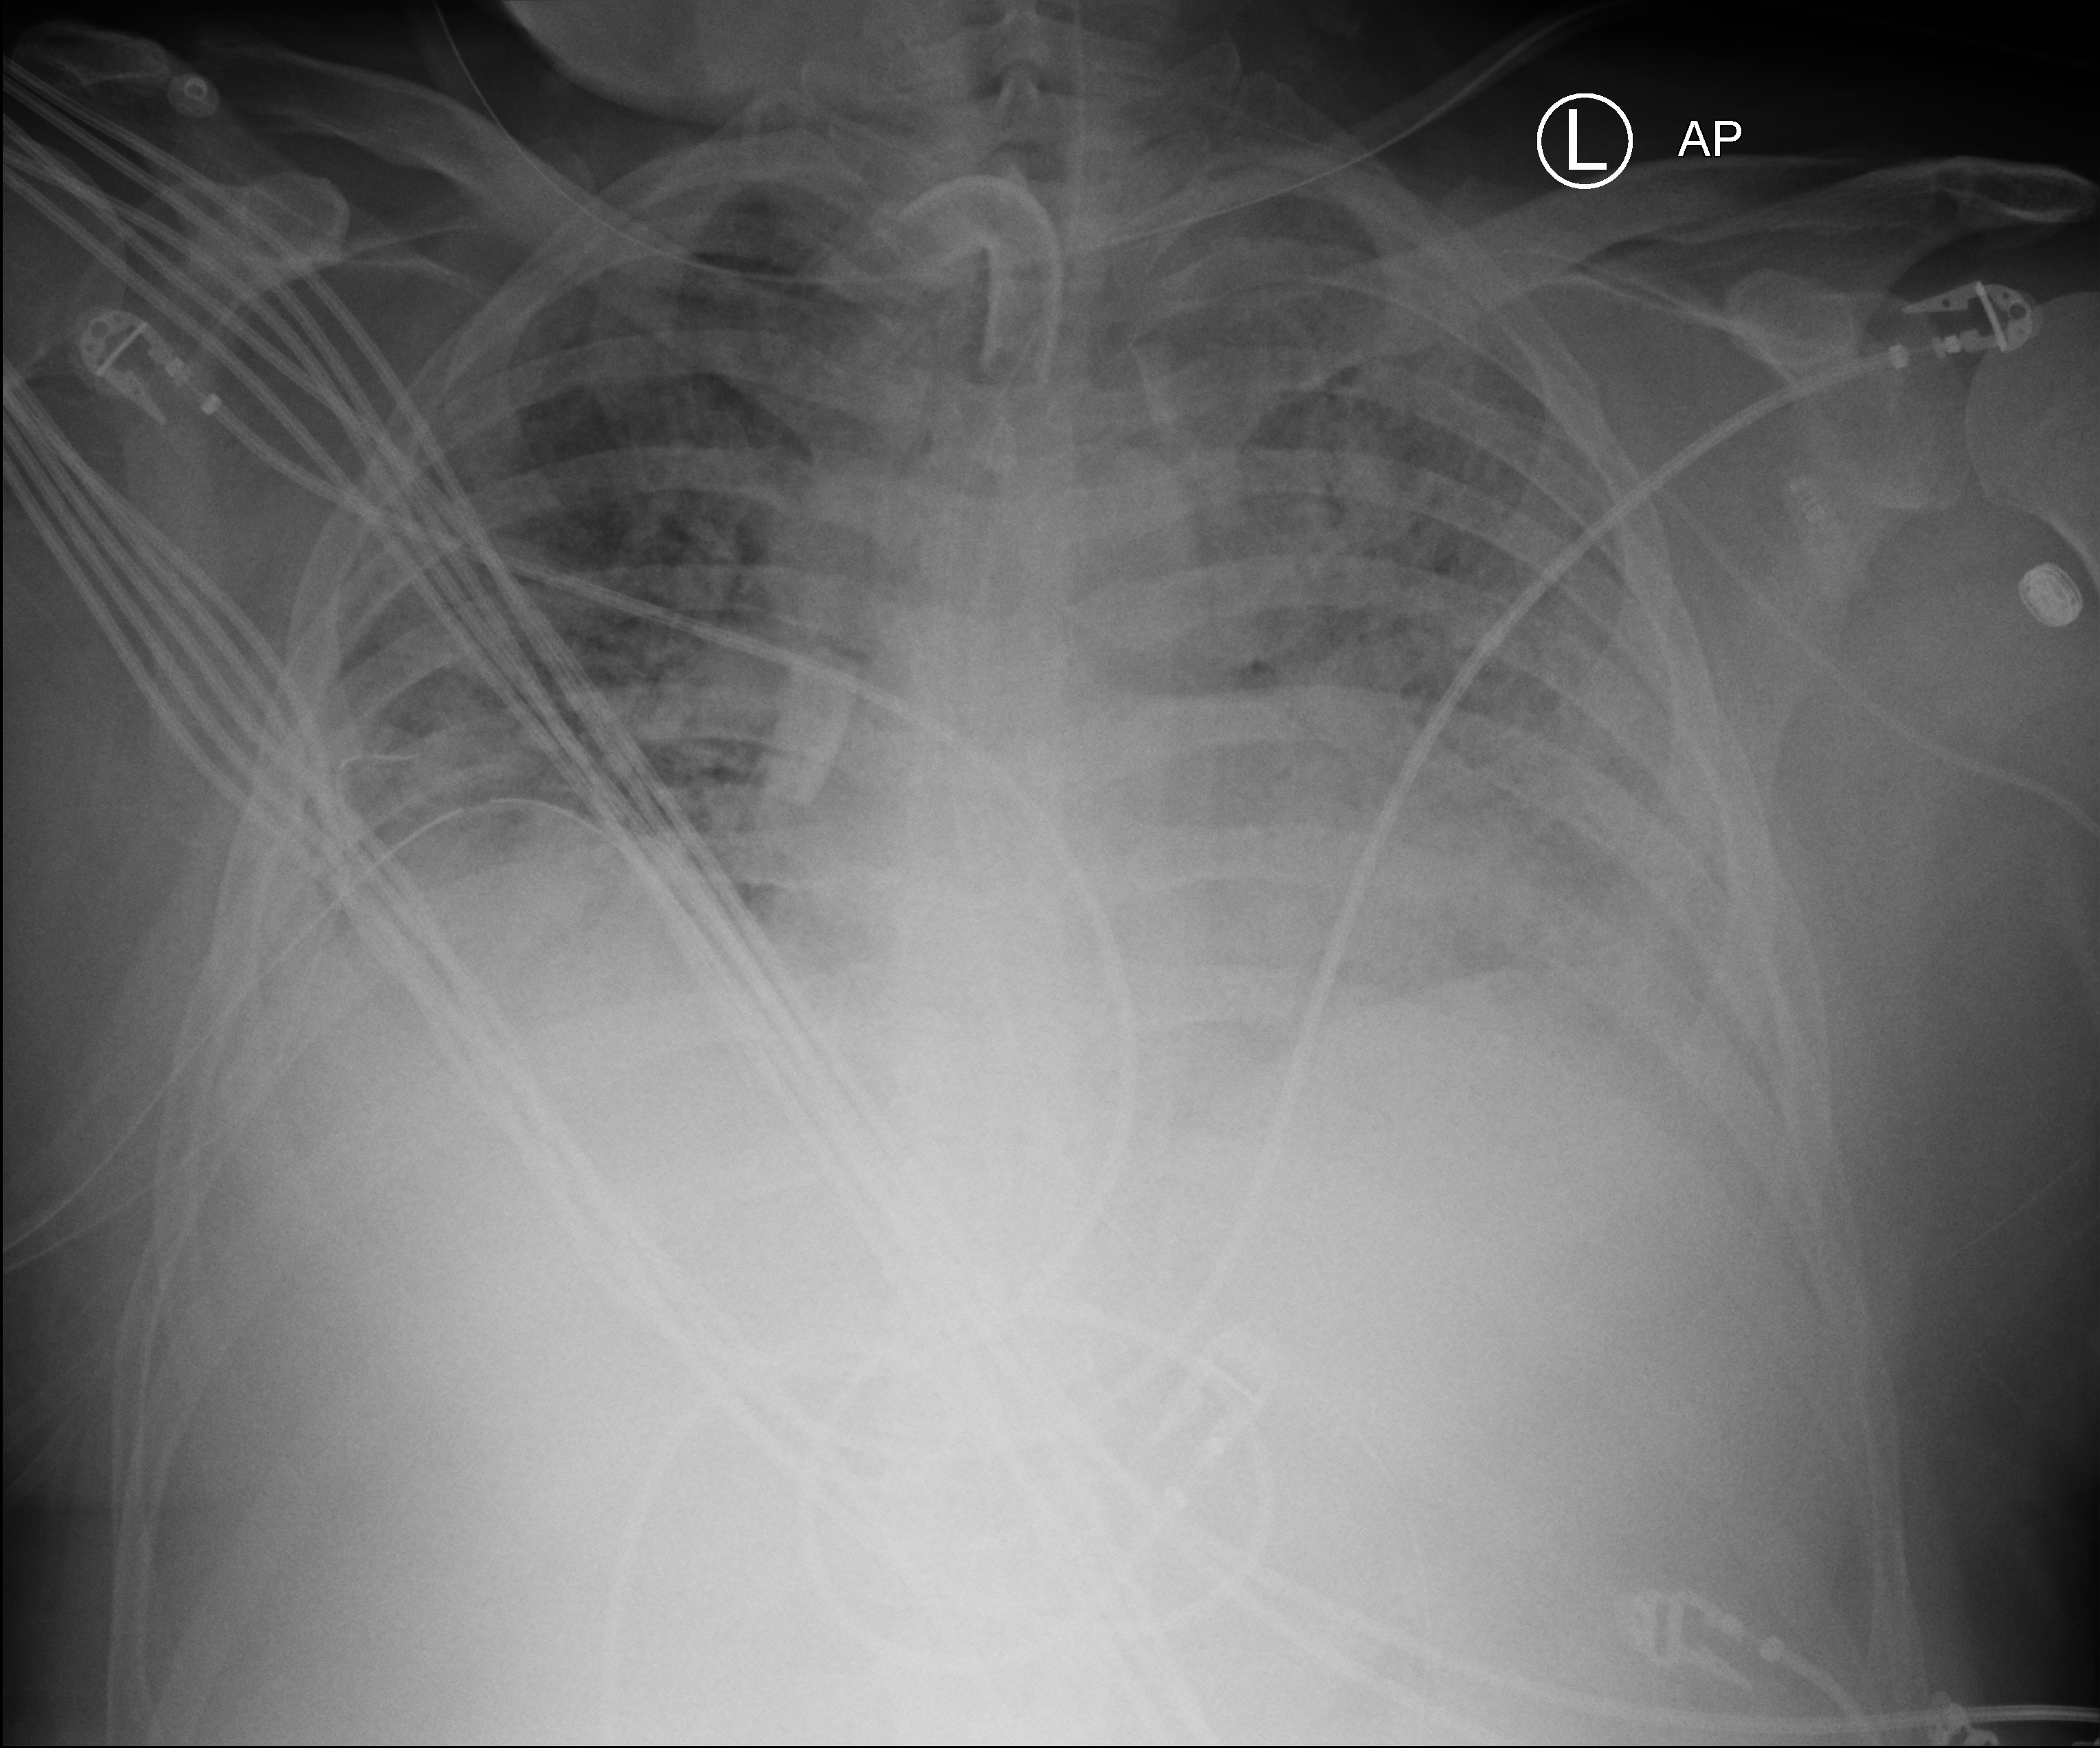
Bedside chest radiograph (computed radiography), anteroposterior (AP) projection. Male patient hospitalised with COVID-19, age 18–59 years.
Admission-level facts for this patient (not findings on this image; timing relative to this image not recorded):
- diabetes (admission record): no
- admitted to intensive care during this hospital stay: yes